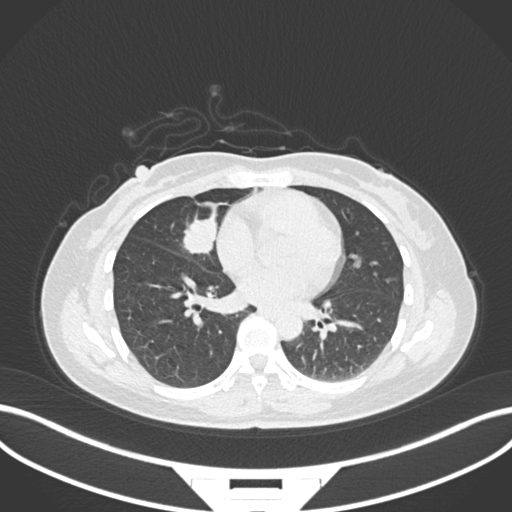
Chest CT, one axial slice; slice 70 of 171 in the series (ordered by position); reconstruction kernel B30f; 120 kVp; lung window (W 1500 / L -600 HU); 1 mm slice thickness; 512 × 512 image matrix, field of view 400 × 400 mm. Female patient, age 43 years. From the clinical record (not read from this slice): clinical TNM (as recorded): T1c N3 M1; histopathological grade: G1.
Structures marked on this image (rectangle marked by the reading radiologist):
- lung tumour (recorded histology: adenocarcinoma): box from (x=177, y=212) to (x=220, y=259) px